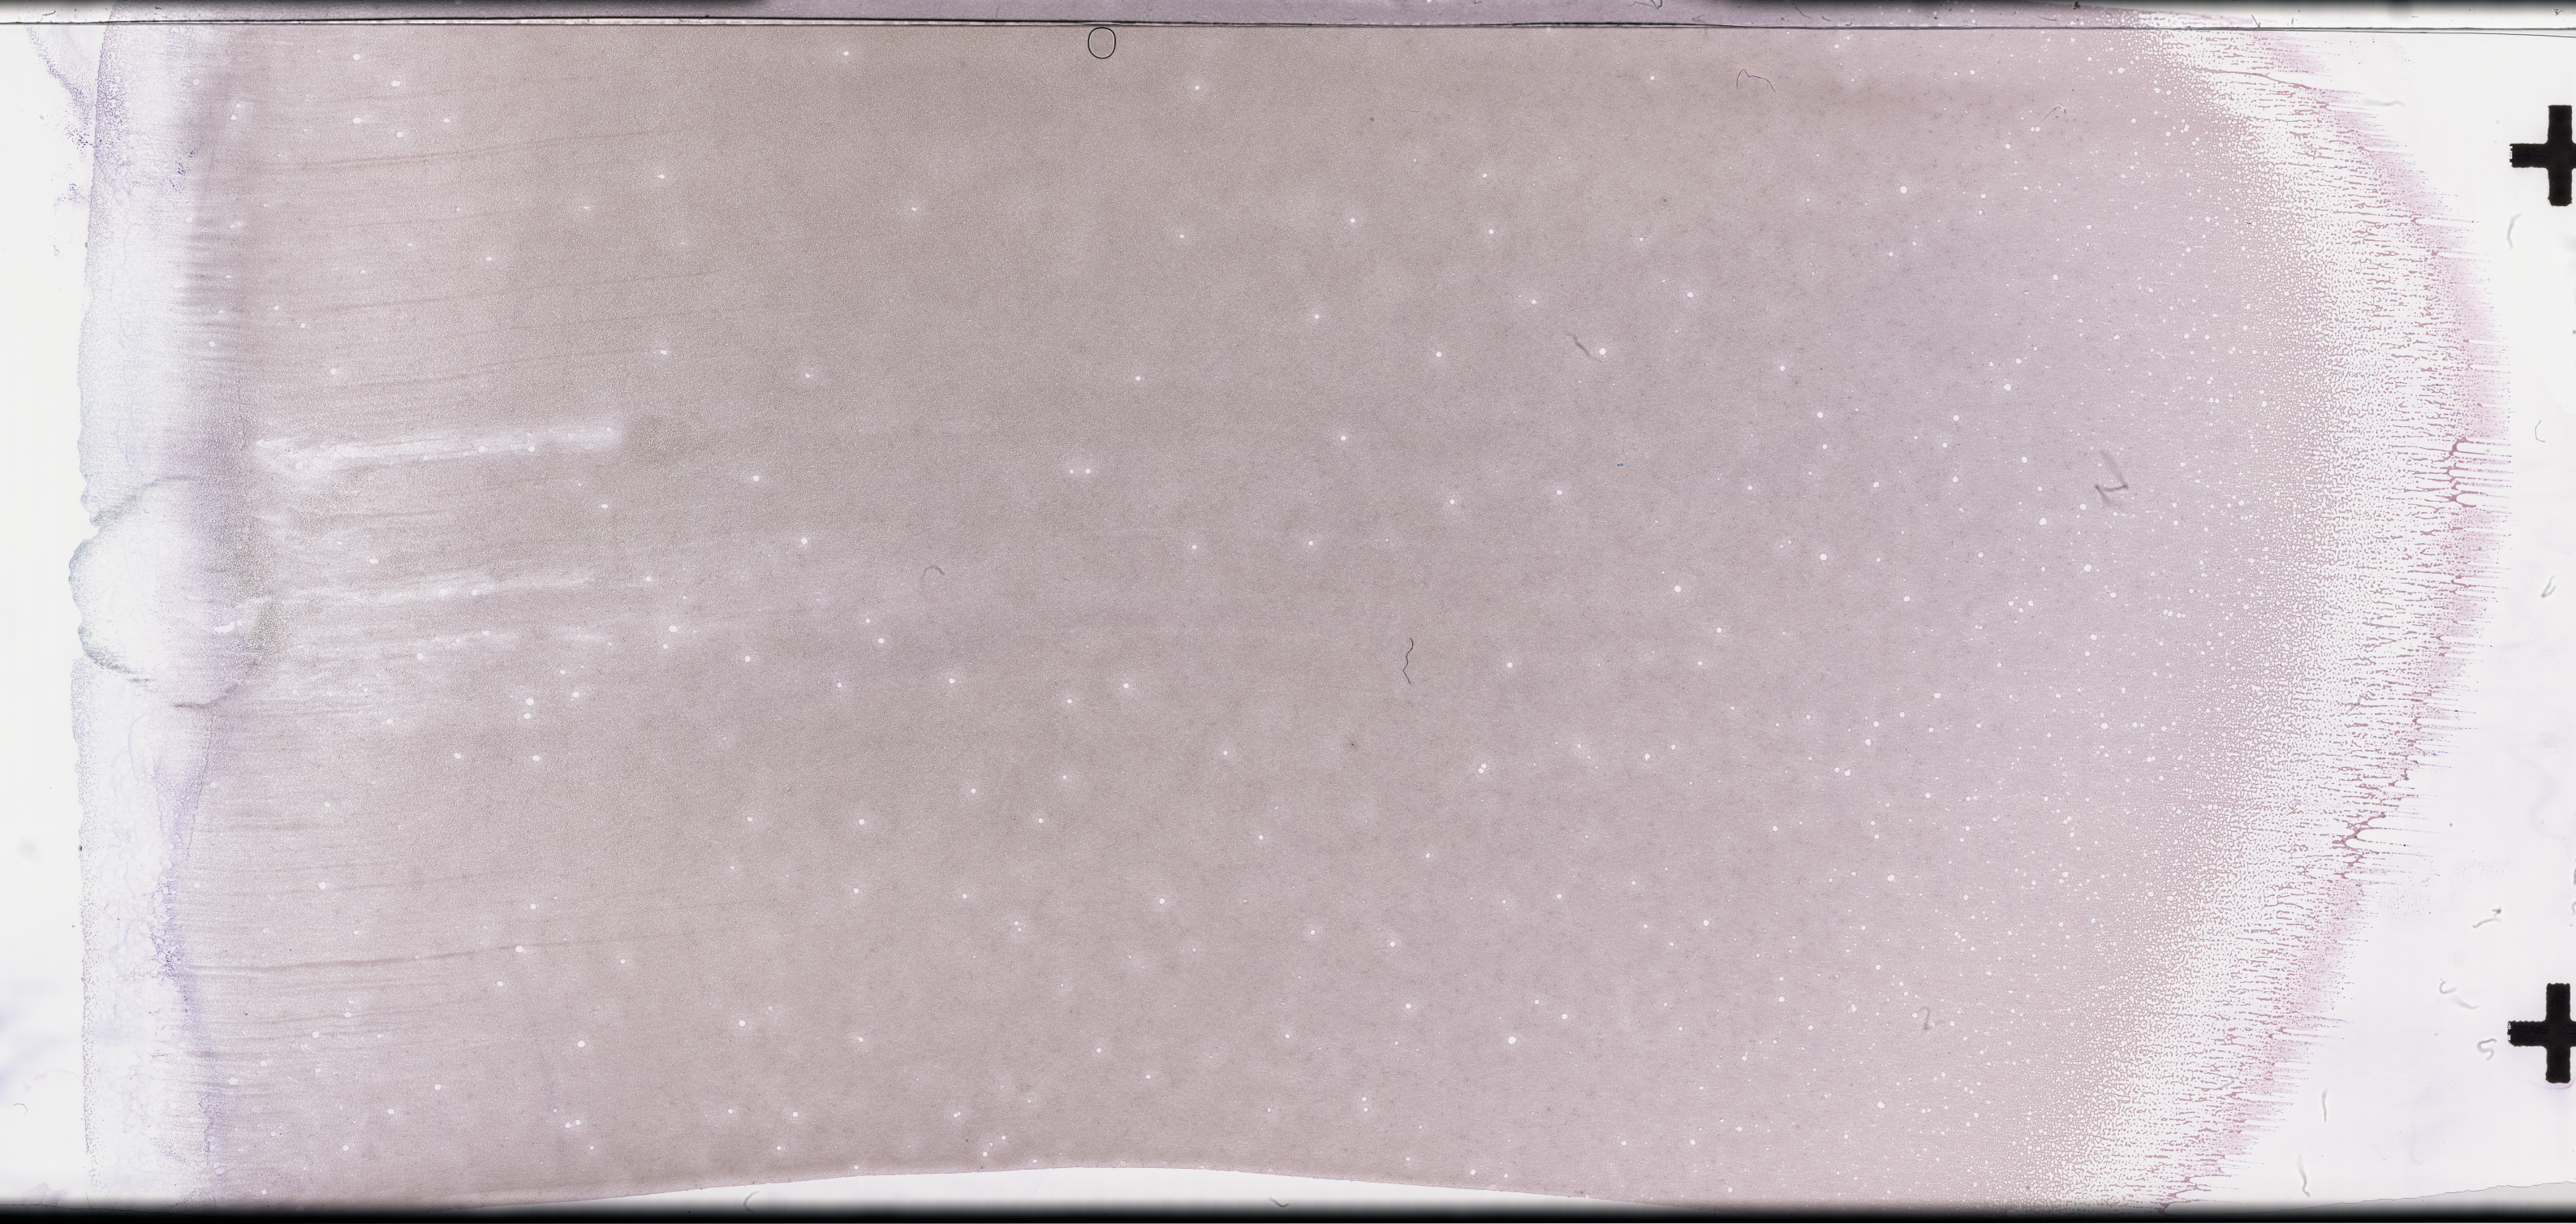
Whole-slide image of a whole blood smear, Wright-Giemsa stain, low-resolution overview of the scanned area, about 51.3 x 24.4 mm; EDTA-anticoagulated smear; specimen time point: collected on treatment. Patient sex: female.
Patient diagnosis: Plasma Cell Myeloma.